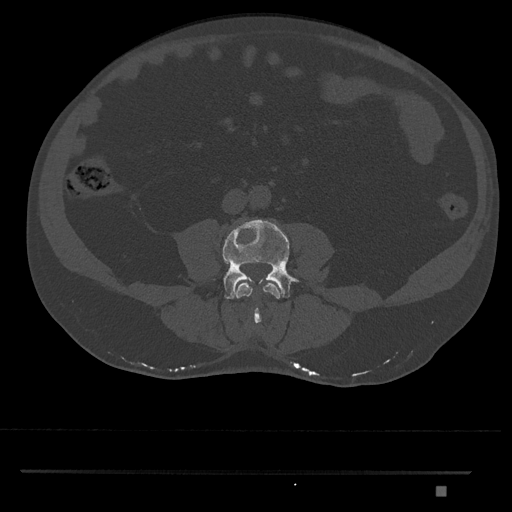
CT including the spine, one axial slice. Slice 638 of 1134 in the series (ordered by position). Bone window (W 1800 / L 400 HU). 512 × 512 image matrix, field of view 429 × 429 mm. Male patient, age 65 years. From the clinical record (not read from this slice): primary cancer: prostate.
Annotated regions visible in this slice (semi-automatic segmentation, software-assisted and operator-edited):
- L3 vertebra: bounding box (x1, y1, x2, y2) in pixels: (236, 281, 280, 324)
- L4 vertebra: (222, 219, 299, 299)